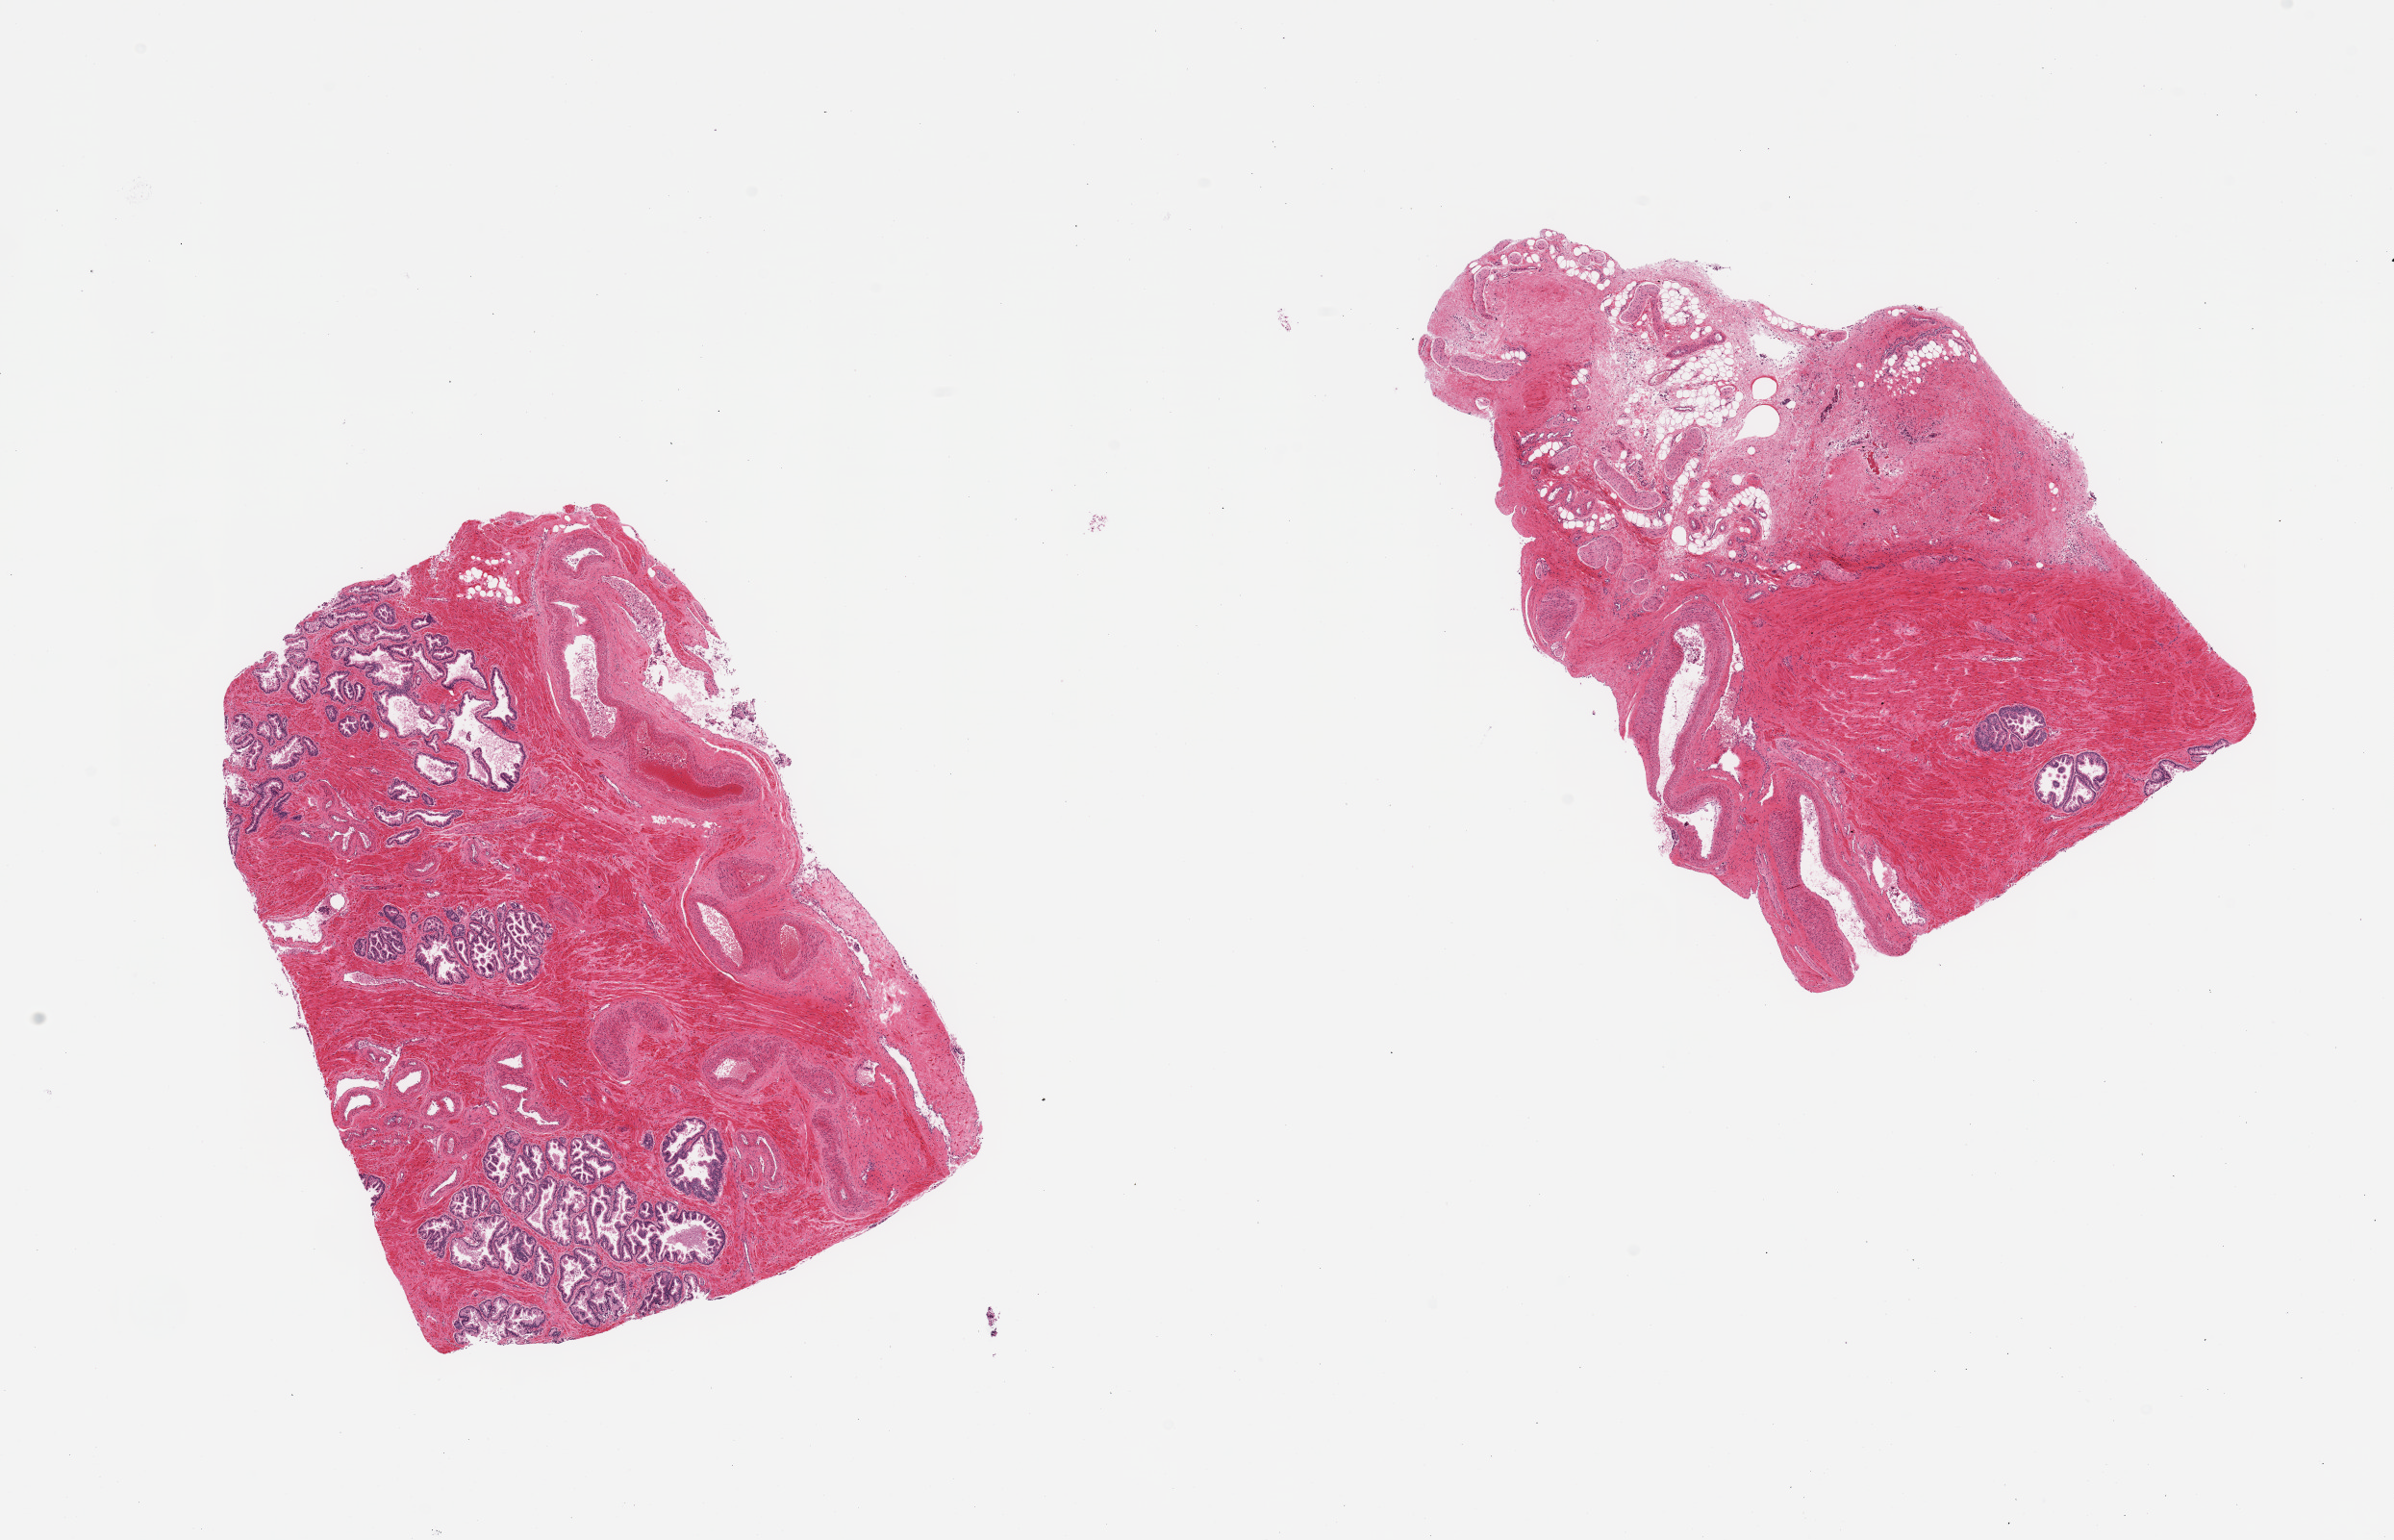
Haematoxylin and eosin whole-slide image, brightfield — low-resolution overview of the scanned area, about 19.7 x 12.7 mm. PAXgene-fixed, paraffin-embedded tissue. Section of prostate (target tissue). Donor tissue sample. Male donor.
Review note (as recorded): 2 pieces, hyperplastic glandular pattern.